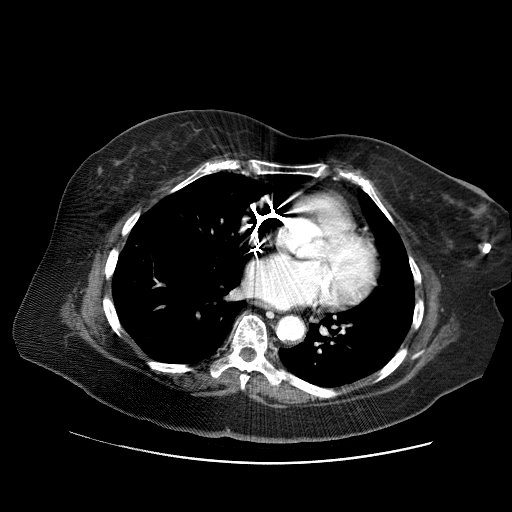
Contrast-enhanced abdominal CT (liver protocol), one axial slice; position 69 of 71 along the scan axis; 120 kVp; soft-tissue window (W 400 / L 40 HU); 2.5 mm slice thickness; 512 × 512 image matrix. Case-level facts recorded for this patient, not image findings: diagnosis: hepatocellular carcinoma (patient treated with transarterial chemoembolisation; whether this scan precedes or follows treatment is not stated here); TNM stage (as recorded): Stage-II; Child-Pugh class: A; tumour differentiation: poorly differentiated; tumour nodularity: multinodular.
Outlined on this slice (semi-automatic segmentation, software-assisted and operator-edited):
- abdominal aorta: bounding box <277,317,303,340> (left, top, right, bottom; pixels)